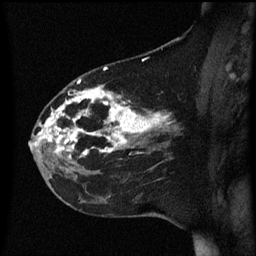
Breast MRI (dynamic contrast-enhanced), one sagittal slice. Slice 23 of 60 in the series (ordered by position). Dynamic contrast-enhanced series, image 2 of 3 at this slice position (ordered by acquisition). 1.5 T. TE 4.2 ms, TR 8.4 ms. 256 × 256 image matrix, field of view 200 × 200 mm. Female patient, age 35 years. From the clinical record (not read from this slice): setting: breast cancer imaged before/during neoadjuvant chemotherapy; receptor status: HER2-positive.
Outlined on this slice (semi-automatic segmentation, software-assisted and operator-edited):
- analysis volume of interest (the breast-tissue region the enhancement analysis was run in; not a lesion): box from (x=32, y=78) to (x=173, y=163) px
- tumour enhancement mask (voxels above the 70 % enhancement threshold inside the analysis volume of interest): (x=32, y=80)–(x=171, y=157)